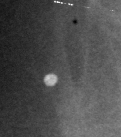
Region of interest cut from a scanned film mammogram (one marked finding), right breast, MLO view, BI-RADS breast density category 3 (scale 1–4).
Calcifications, morphology lucent center; BI-RADS assessment category 2; subtlety rating 3 on a 1 (subtle) to 5 (obvious) scale; benign; no additional work-up was recommended (benign without callback).